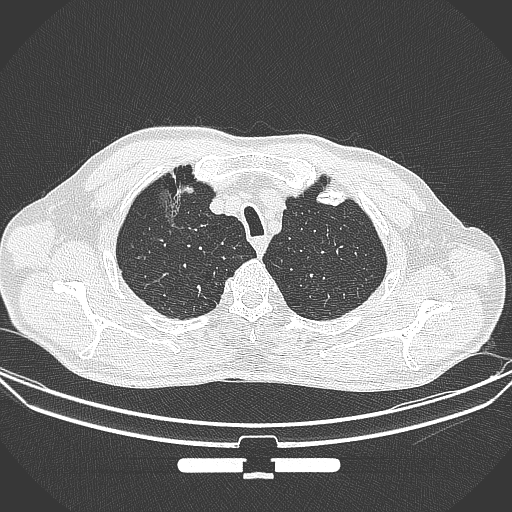
Chest CT, one axial slice; 120 kVp; lung window (W 1500 / L -600 HU); 1 mm slice thickness; 512 × 512 image matrix. Male patient, age 67 years. Case-level facts recorded for this patient, not image findings: clinical TNM (as recorded): T1c N0 M0; histopathological grade: G2.
Structures marked on this image (bounding box drawn by a radiologist):
- lung tumour (recorded histology: adenocarcinoma): bounding box <154,187,192,236> (left, top, right, bottom; pixels)